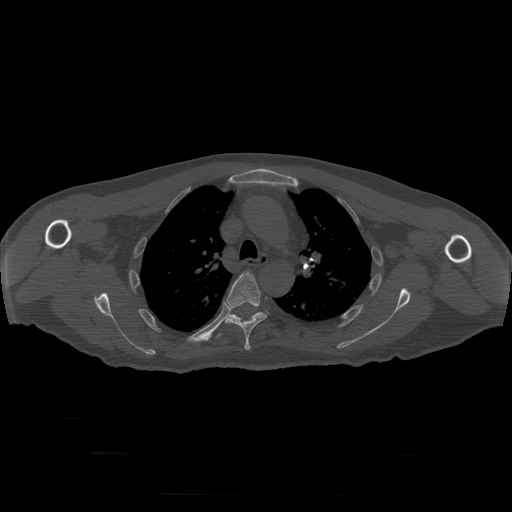
CT including the spine, one axial slice. Position 221 of 397 along the scan axis. 120 kVp. Bone window (W 1800 / L 400 HU). 512 × 512 image matrix, field of view 510 × 510 mm. Patient age 73 years. Case-level facts recorded for this patient, not image findings: primary cancer: prostate.
Structures marked on this image (semi-automatically segmented with operator editing):
- T5 vertebra: box from (x=225, y=273) to (x=267, y=351) px
- T6 vertebra: (x=217, y=312)–(x=261, y=337)